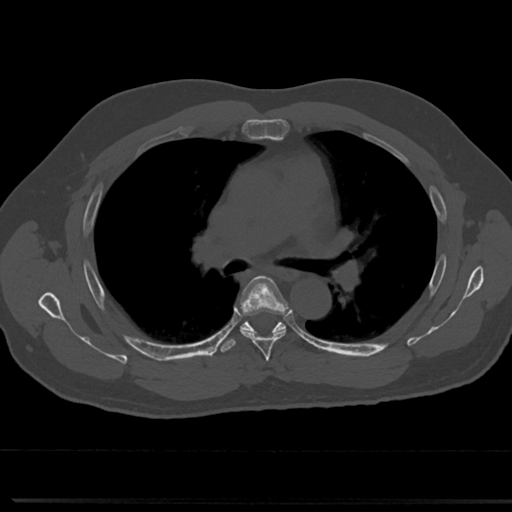
CT including the spine, one axial slice. Position 483 of 817 along the scan axis. Reconstruction kernel Br40s/3. Bone window (W 1800 / L 400 HU). 512 × 512 image matrix, field of view 355 × 355 mm. Male patient, age 61 years. From the clinical record (not read from this slice): primary cancer: prostate.
Outlined on this slice (semi-automatically segmented with operator editing):
- T4 vertebra: bounding box (x1, y1, x2, y2) in pixels: (267, 368, 271, 373)
- T5 vertebra: (238, 278, 288, 355)
- T6 vertebra: (242, 326, 286, 333)